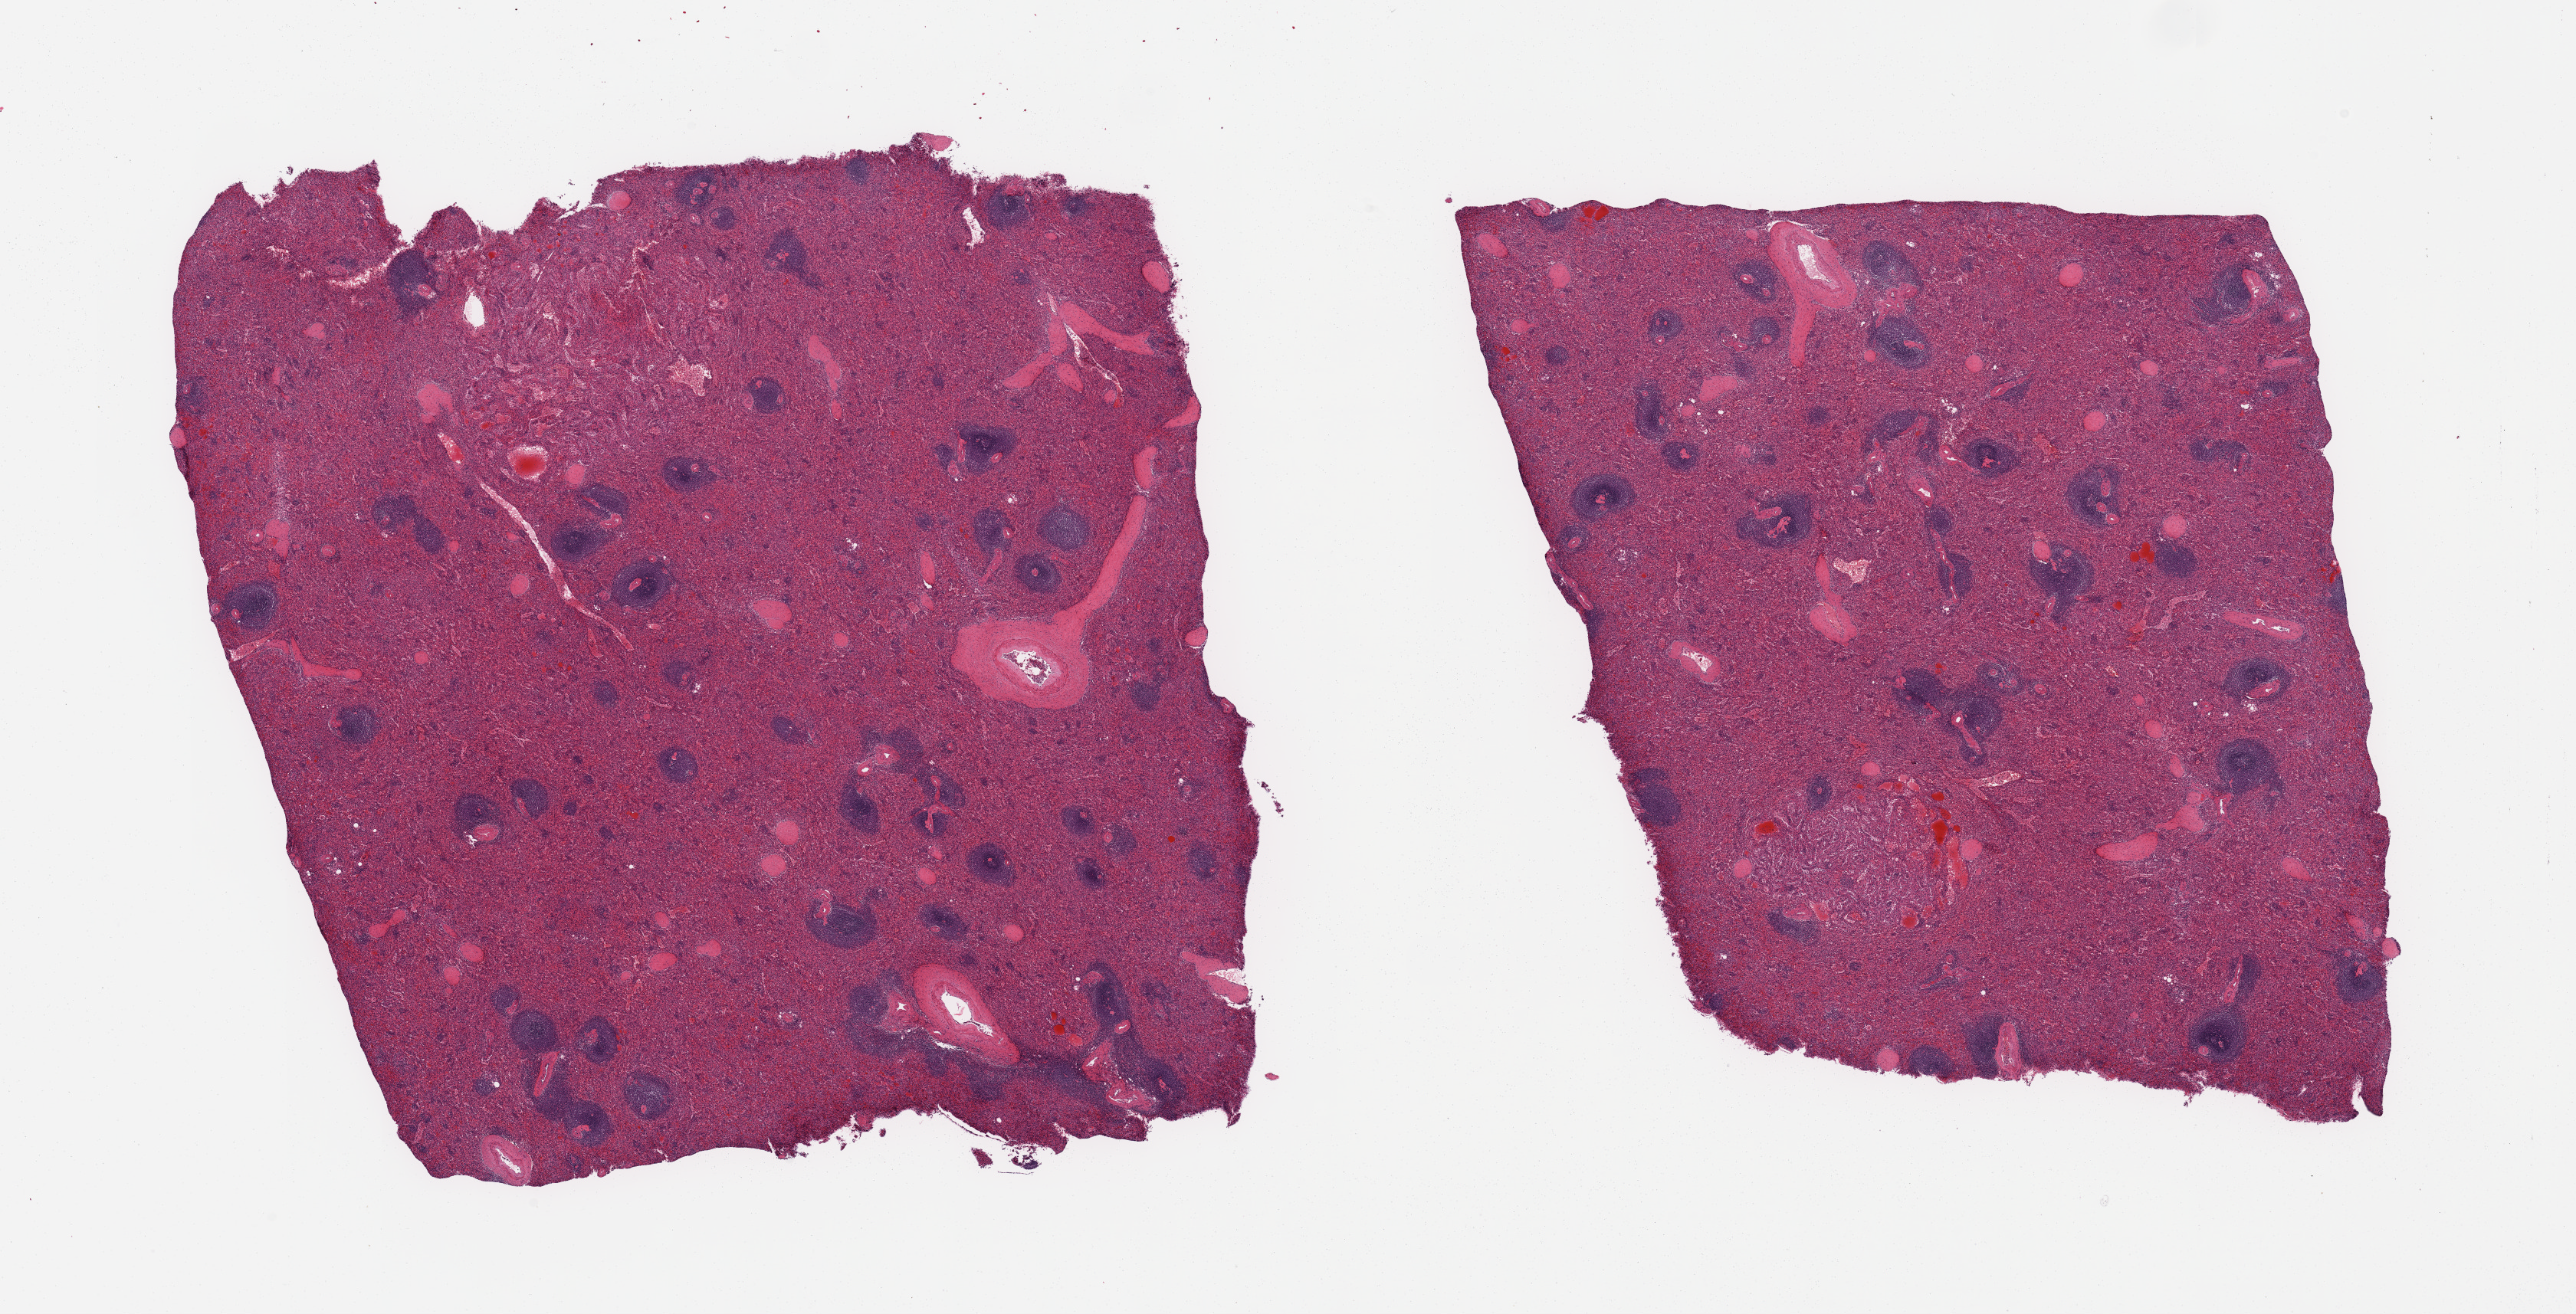
Whole-slide image, haematoxylin and eosin stain, brightfield — shown as a low-resolution overview of the whole scanned area (about 26.6 x 13.6 mm); PAXgene-fixed paraffin-embedded (PFPE) section; sampled site (target tissue): spleen; donor tissue sample. Donor: male.
Review note (as recorded): 2 pieces; slight congestion.